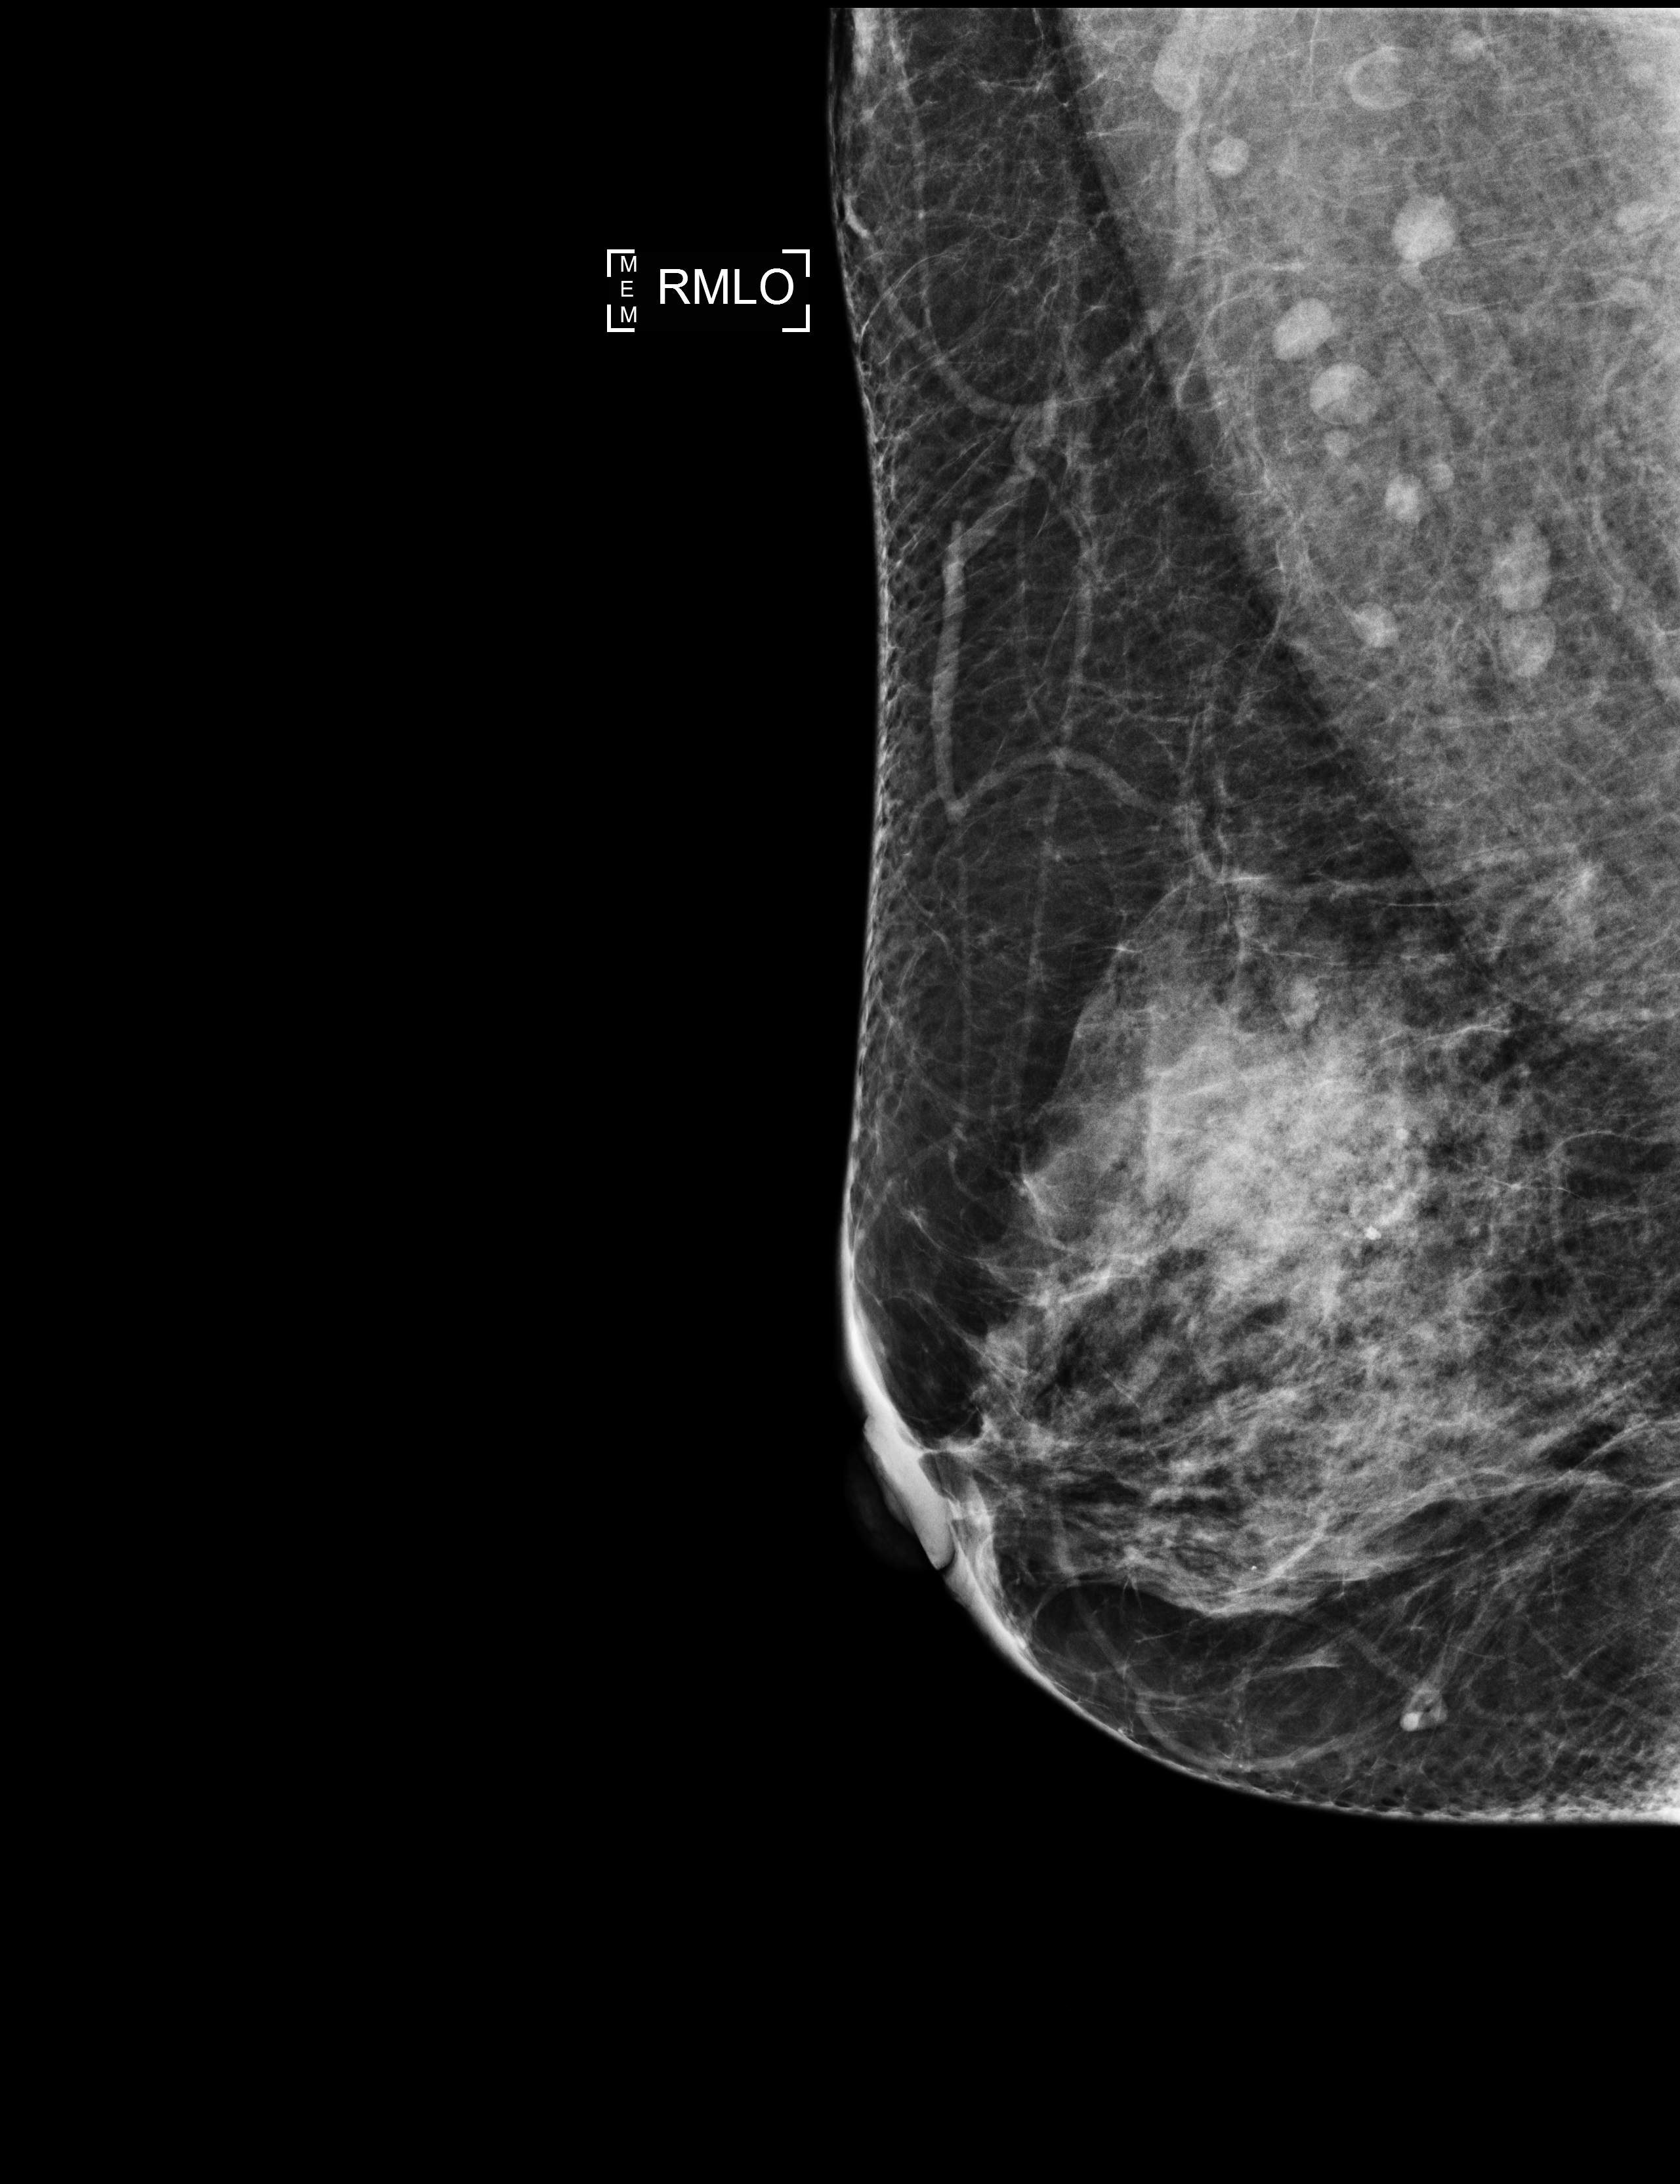
Digital mammogram (FFDM), right breast, MLO view, annual screening mammography examination. Patient aged 57 years (female).
BI-RADS breast density category at the screening exam (both breasts, scale 1–4): 3. Final BI-RADS assessment for this screening round (tomosynthesis exam, both breasts): category 1. Recall: no recall after this screen.